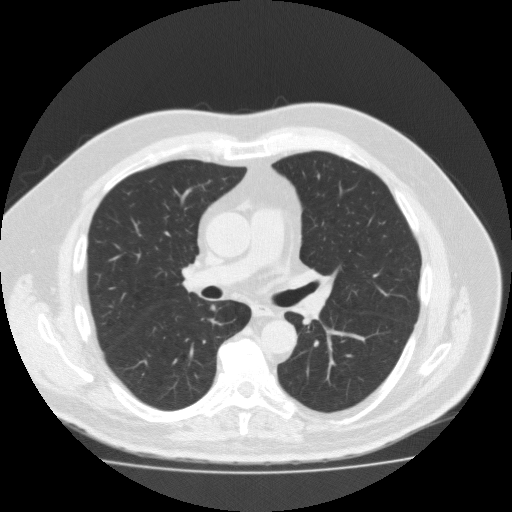
Low-dose screening chest CT, axial slice. Second annual screen. Lung window (W 1500 / L -600 HU). Male participant, aged 56 years at enrolment. Current smoker at enrolment.
Expert reader's lesion annotation, bounding box <198,298,232,324> (left, top, right, bottom; pixels). The exam's reader record, not a measurement of the box and not confirmed to be the same lesion: non-calcified nodule or mass ≥4 mm, right lower lobe, 5 × 5 mm, spiculated (stellate) margins, soft tissue attenuation, pre-existing on the prior screen: no. Lung cancer was diagnosed 448 days after this screen: adenocarcinoma, NOS, right lower lobe, moderately differentiated (G2), stage IA (AJCC 6th edition), 12 mm at pathology.